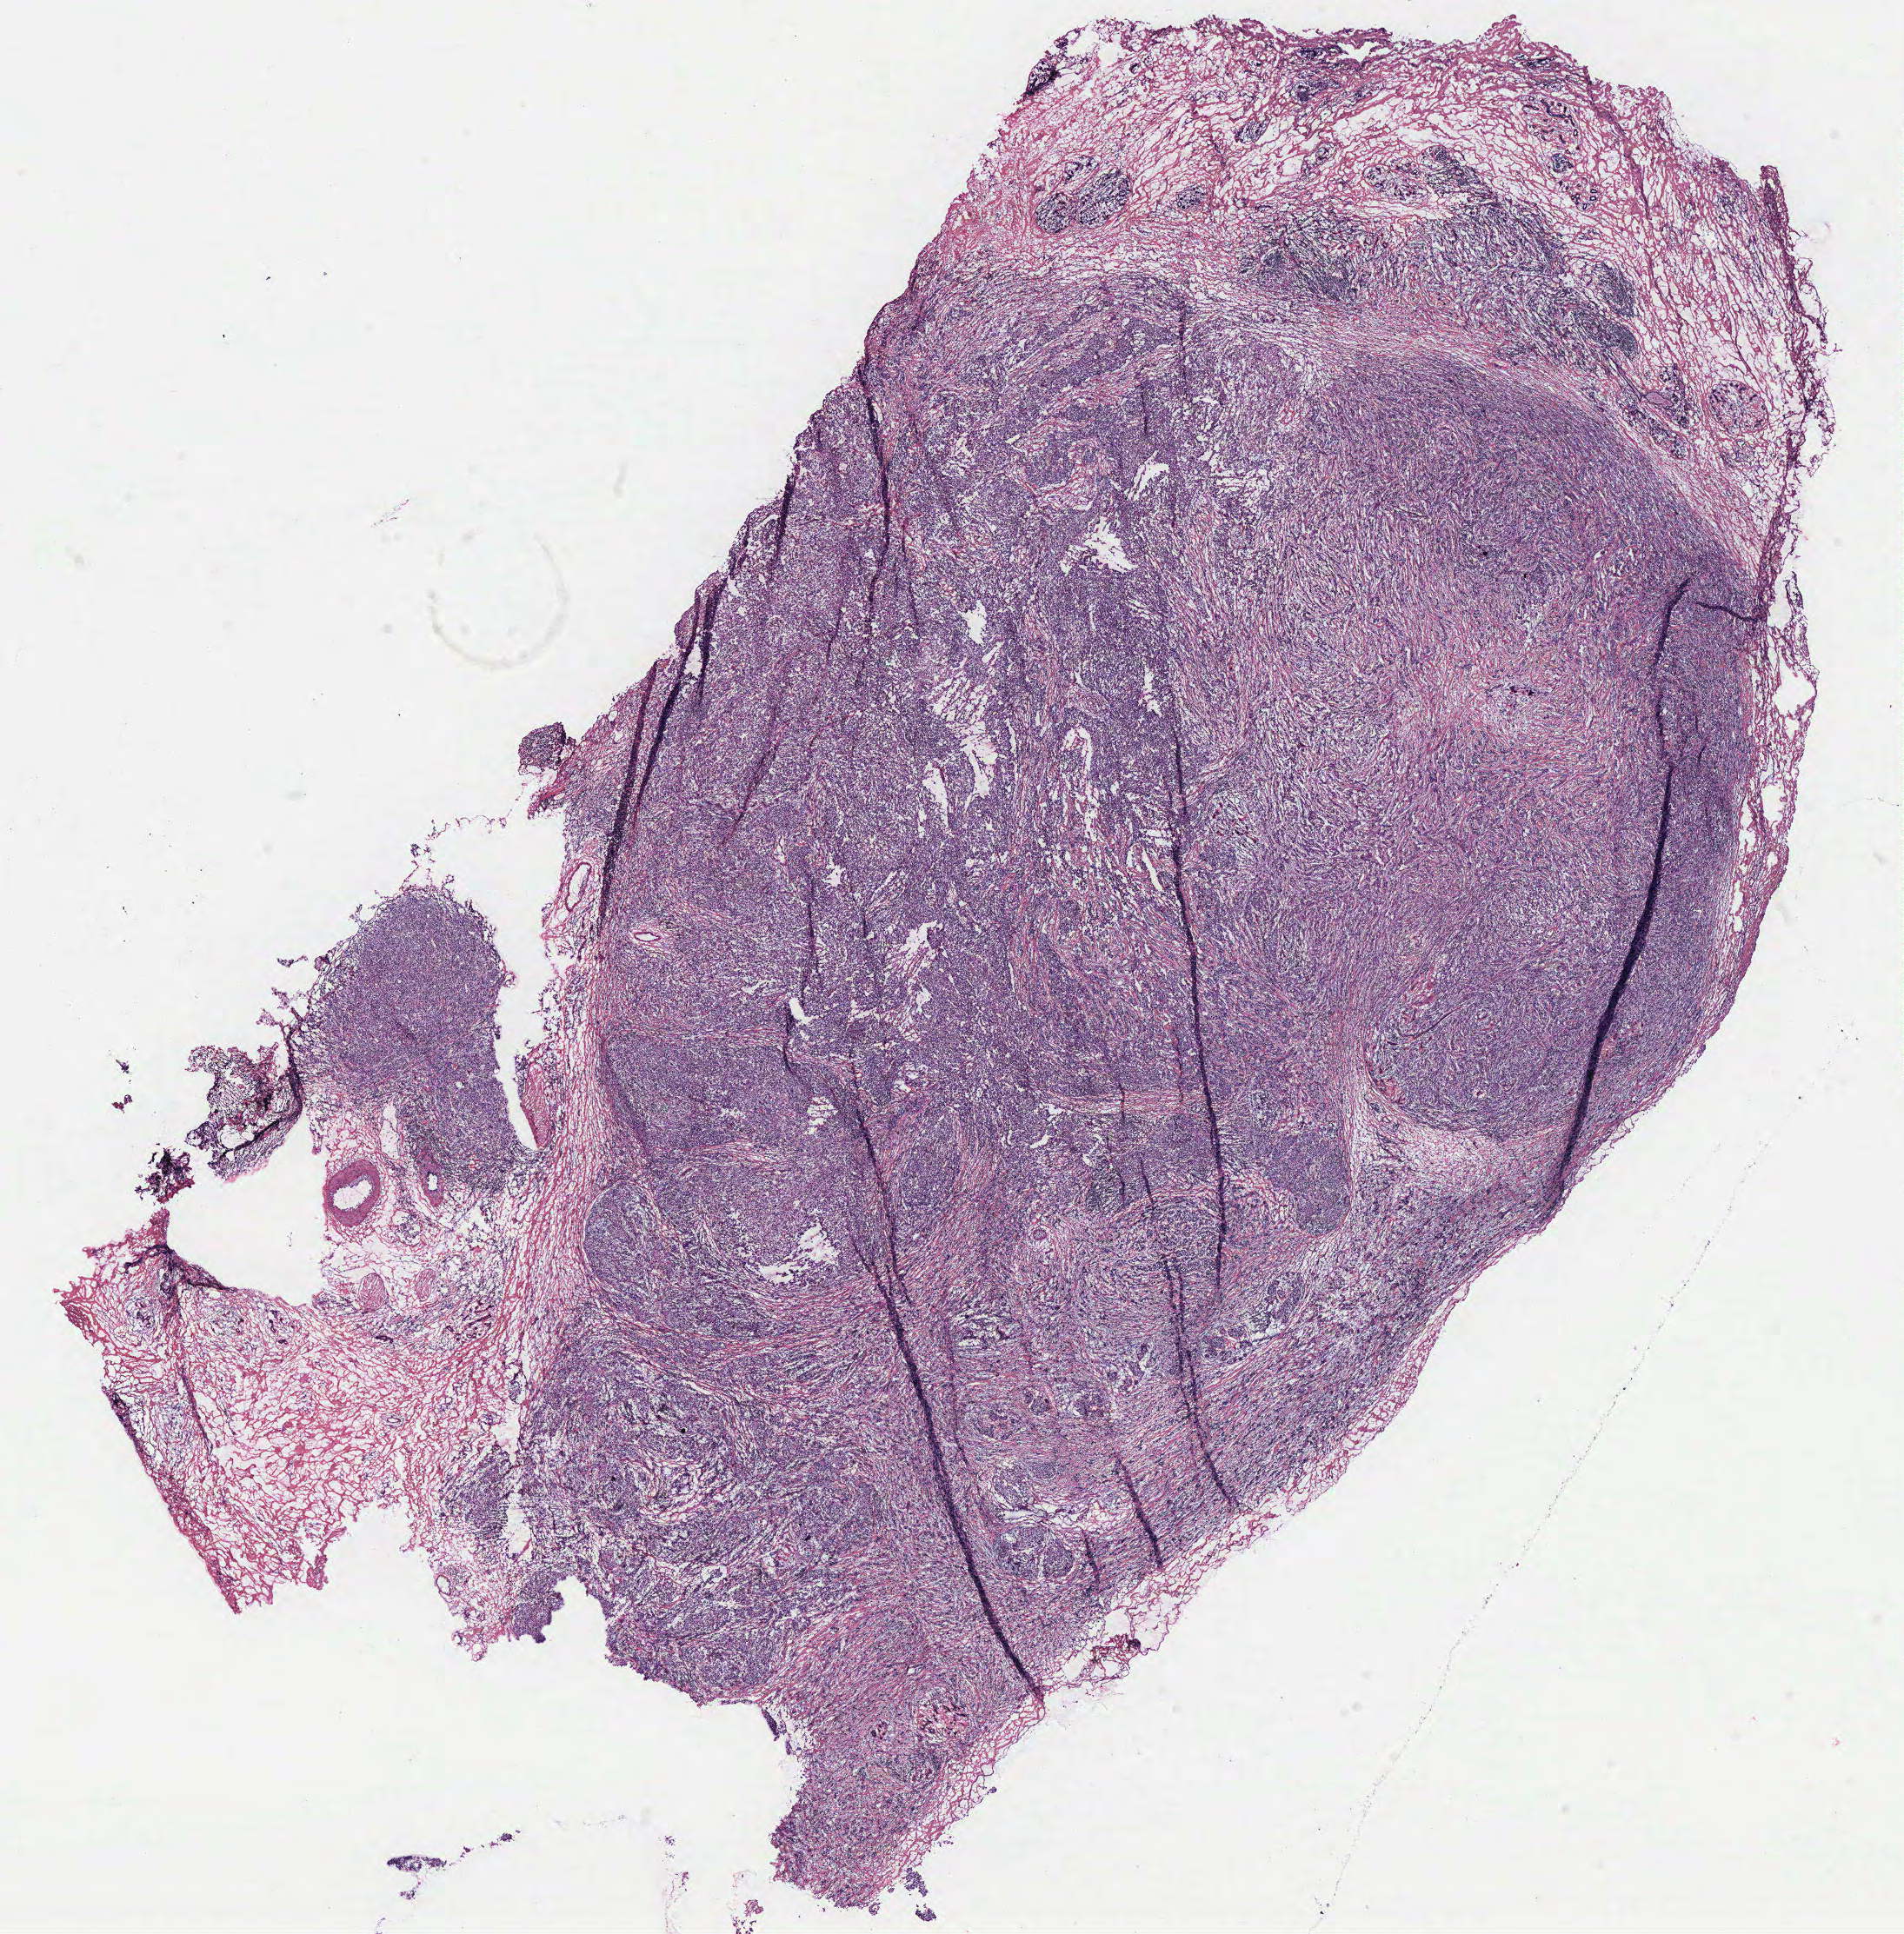
Hematoxylin and eosin (H&E) stained whole-slide image, low-resolution overview of the scanned area, about 17.5 x 17.8 mm; breast, tumour tissue. Female, 30 y/o.
• diagnosis: Infiltrating duct carcinoma, NOS
• AJCC pathologic stage: IIA